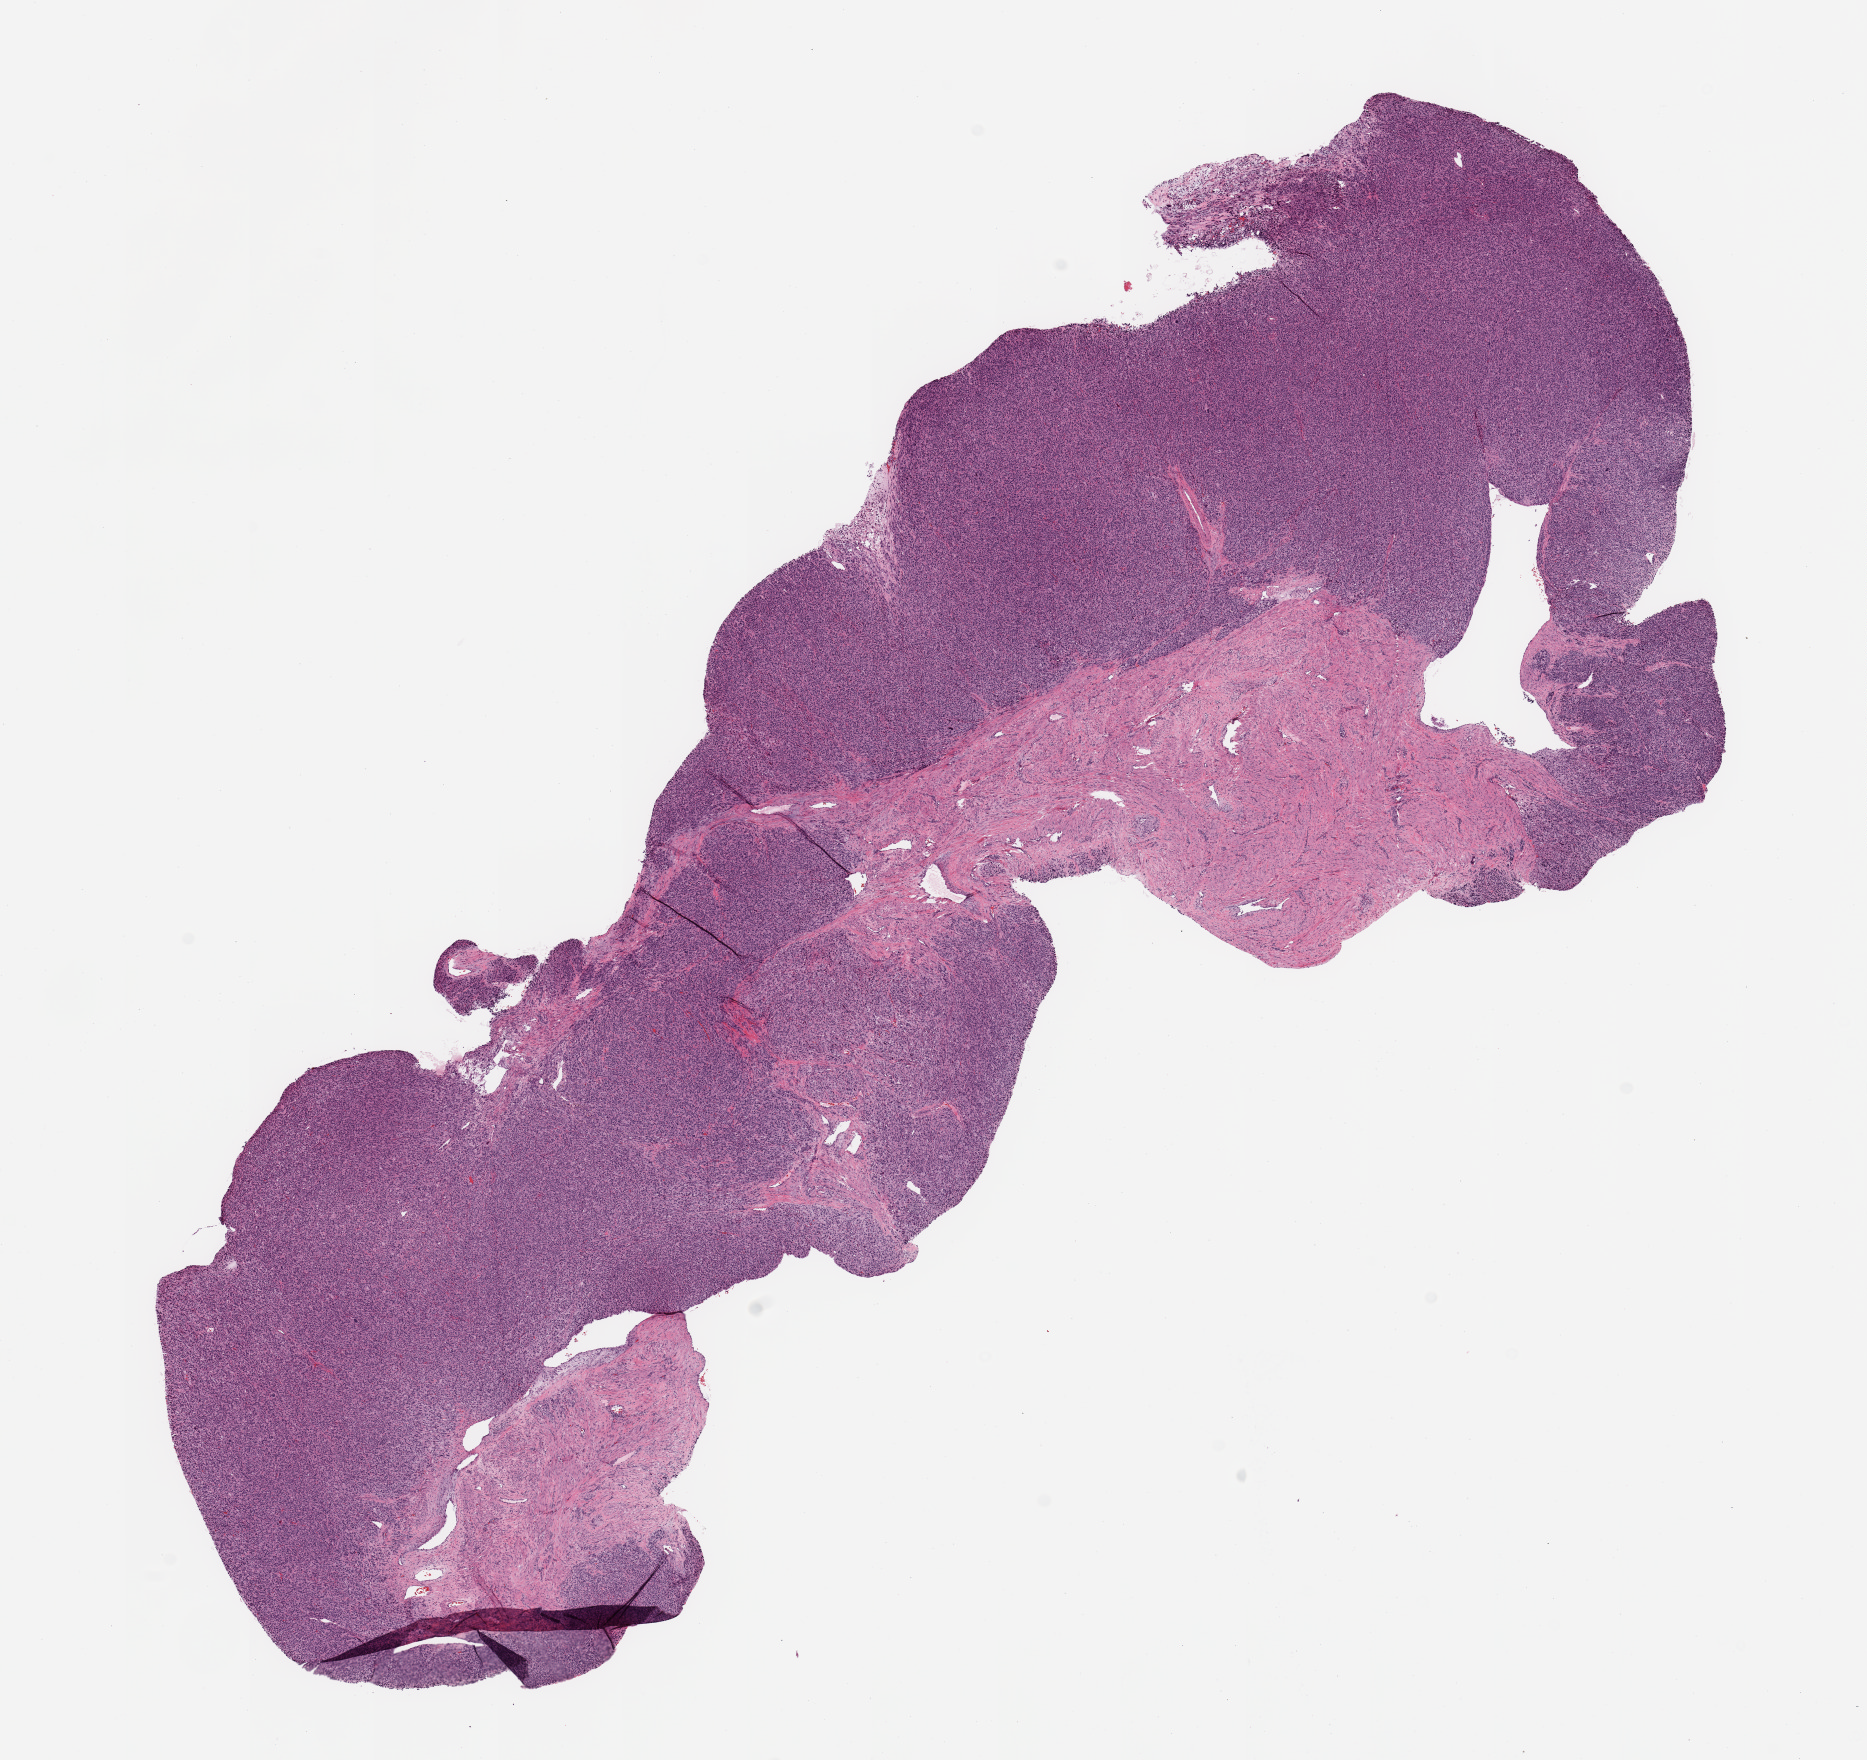
Digitized Hematoxylin and eosin (H&E) stained tissue section (whole slide) — low-resolution overview of the scanned area, about 14.8 x 13.9 mm (slide scanned at 20x). Female, 60 y/o.
Primary tumour site (as recorded): gynecologic. Patient diagnosis (cohort enrolment): sarcoma (site not recorded at cohort level).